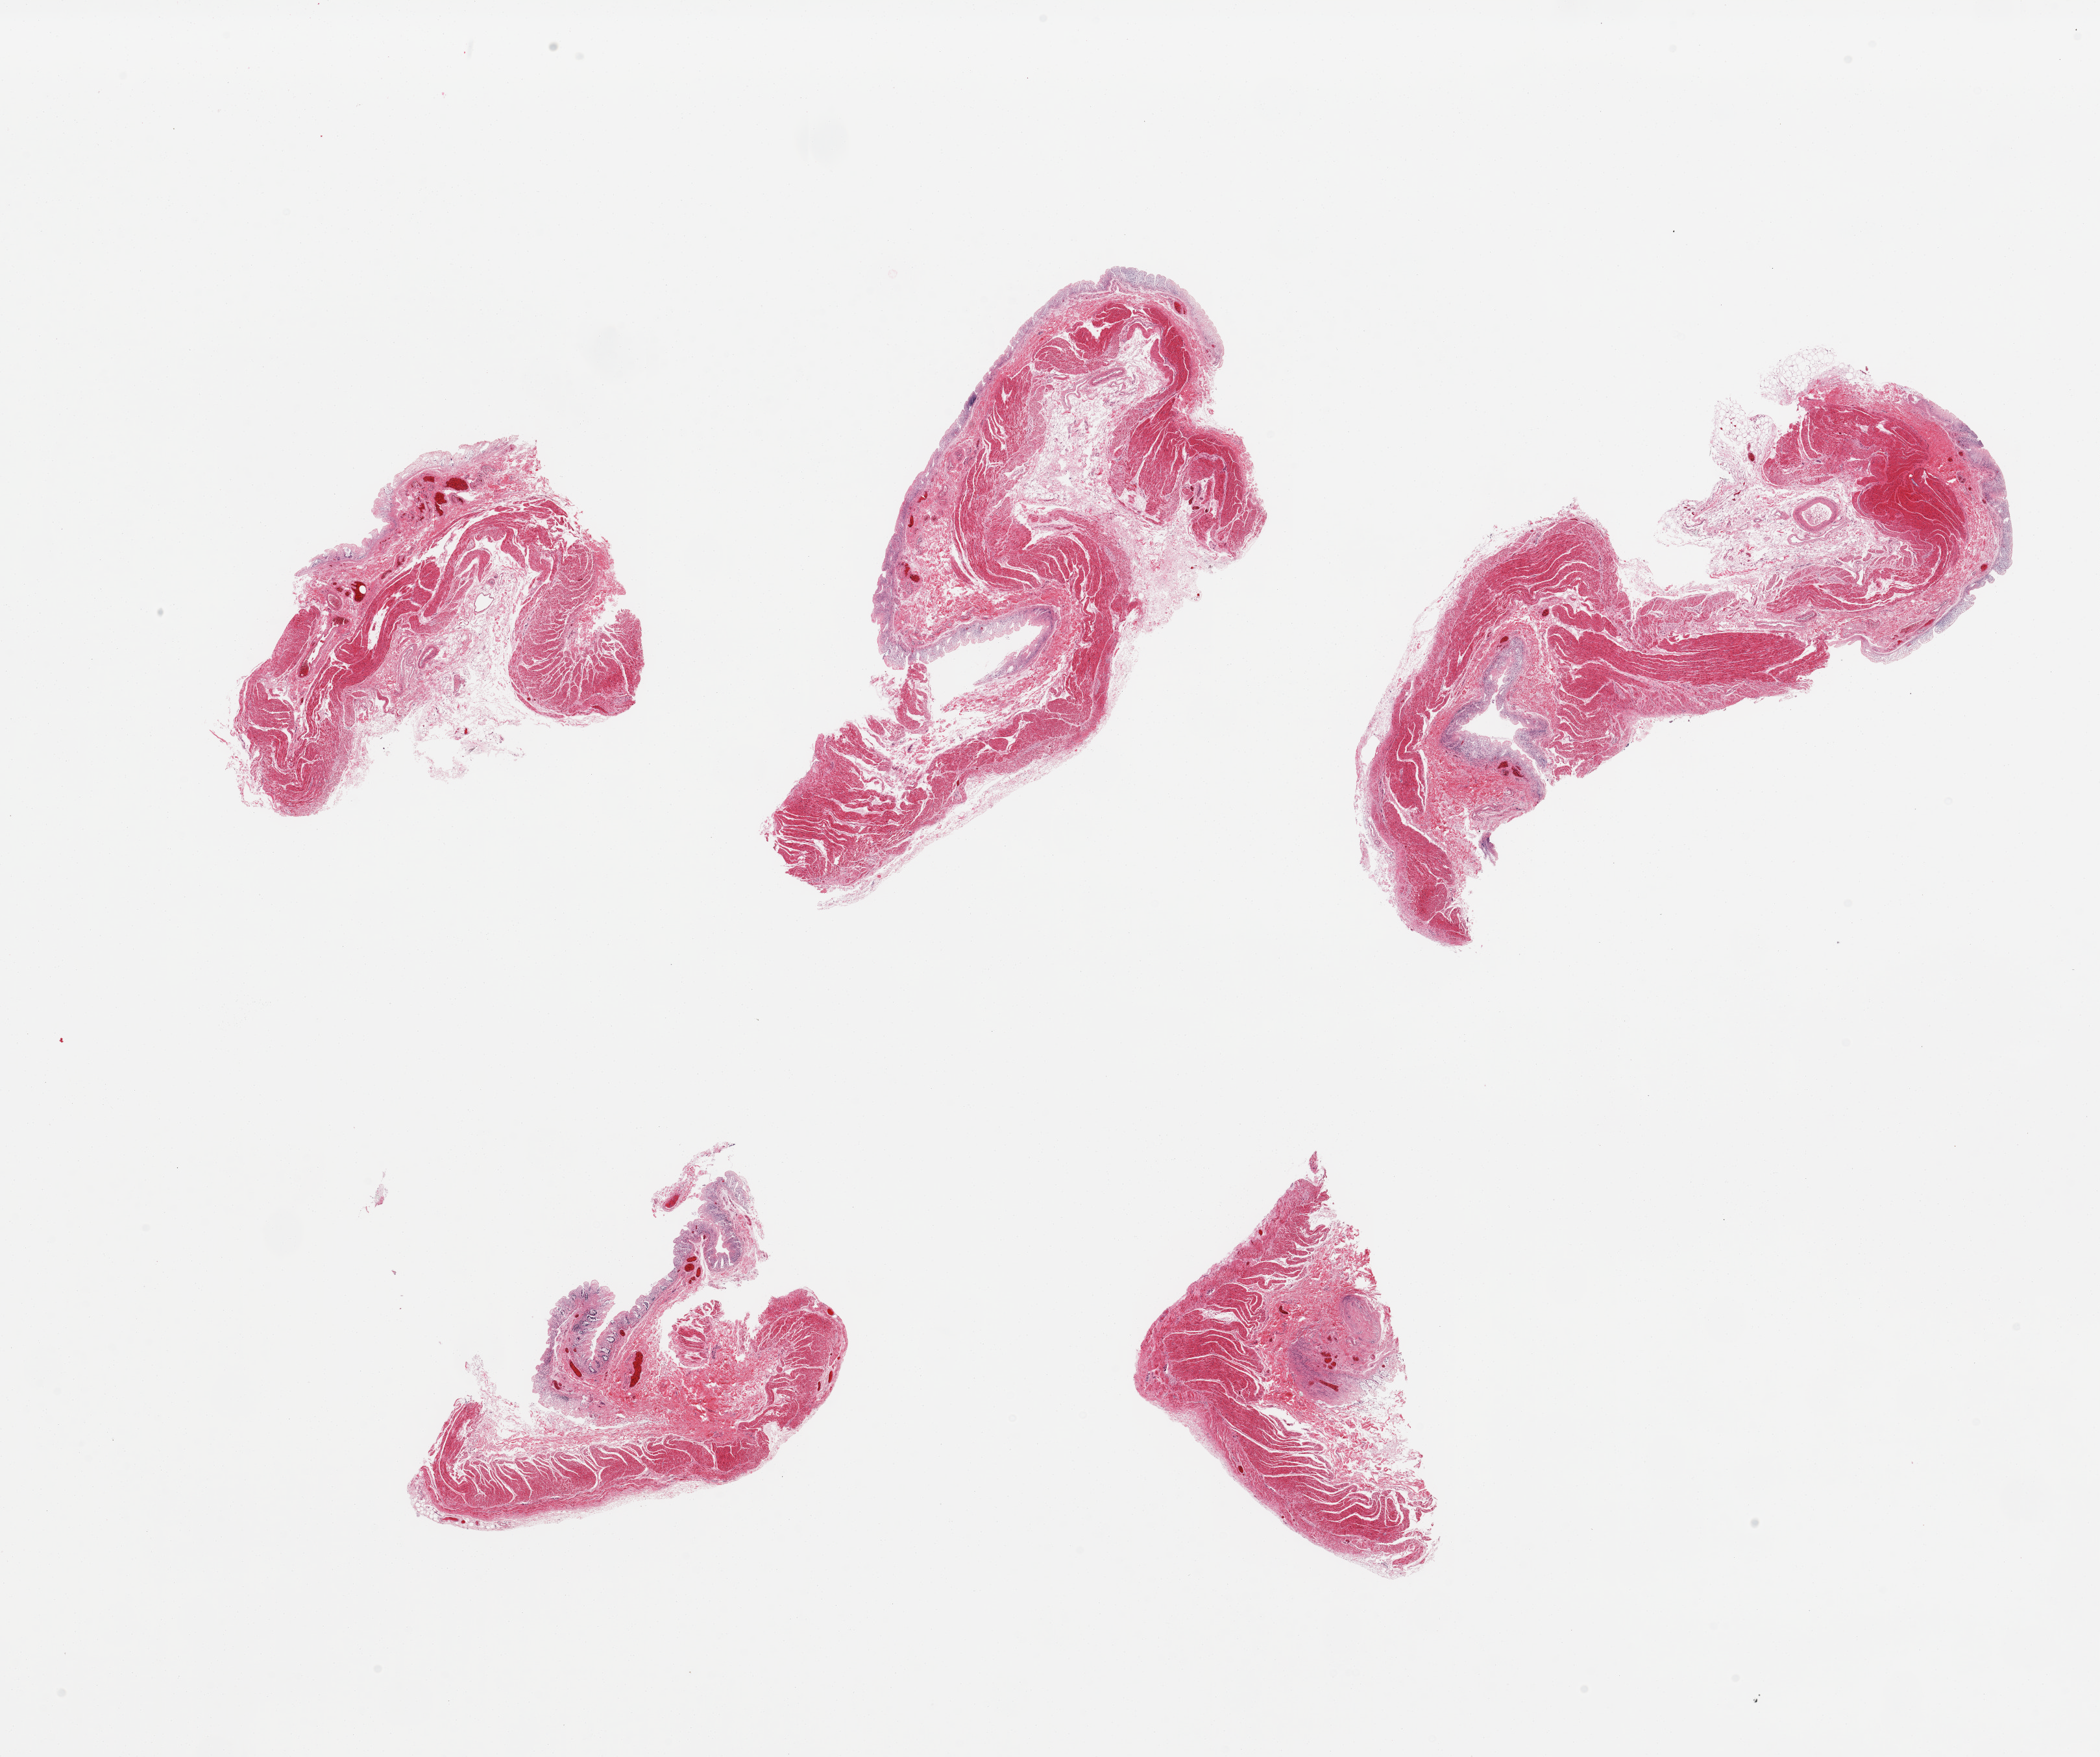
Digitized haematoxylin and eosin-stained section, whole scanned area (about 25.6 x 21.4 mm, slide scanned at 20x) shown as a low-resolution overview. PAXgene-fixed, paraffin-embedded tissue. Target tissue: transverse colon. Tissue donor sample. Male donor.
Pathologist's review note for this sample: 6 pieces; full thickness sections, autolyzed mucosa.